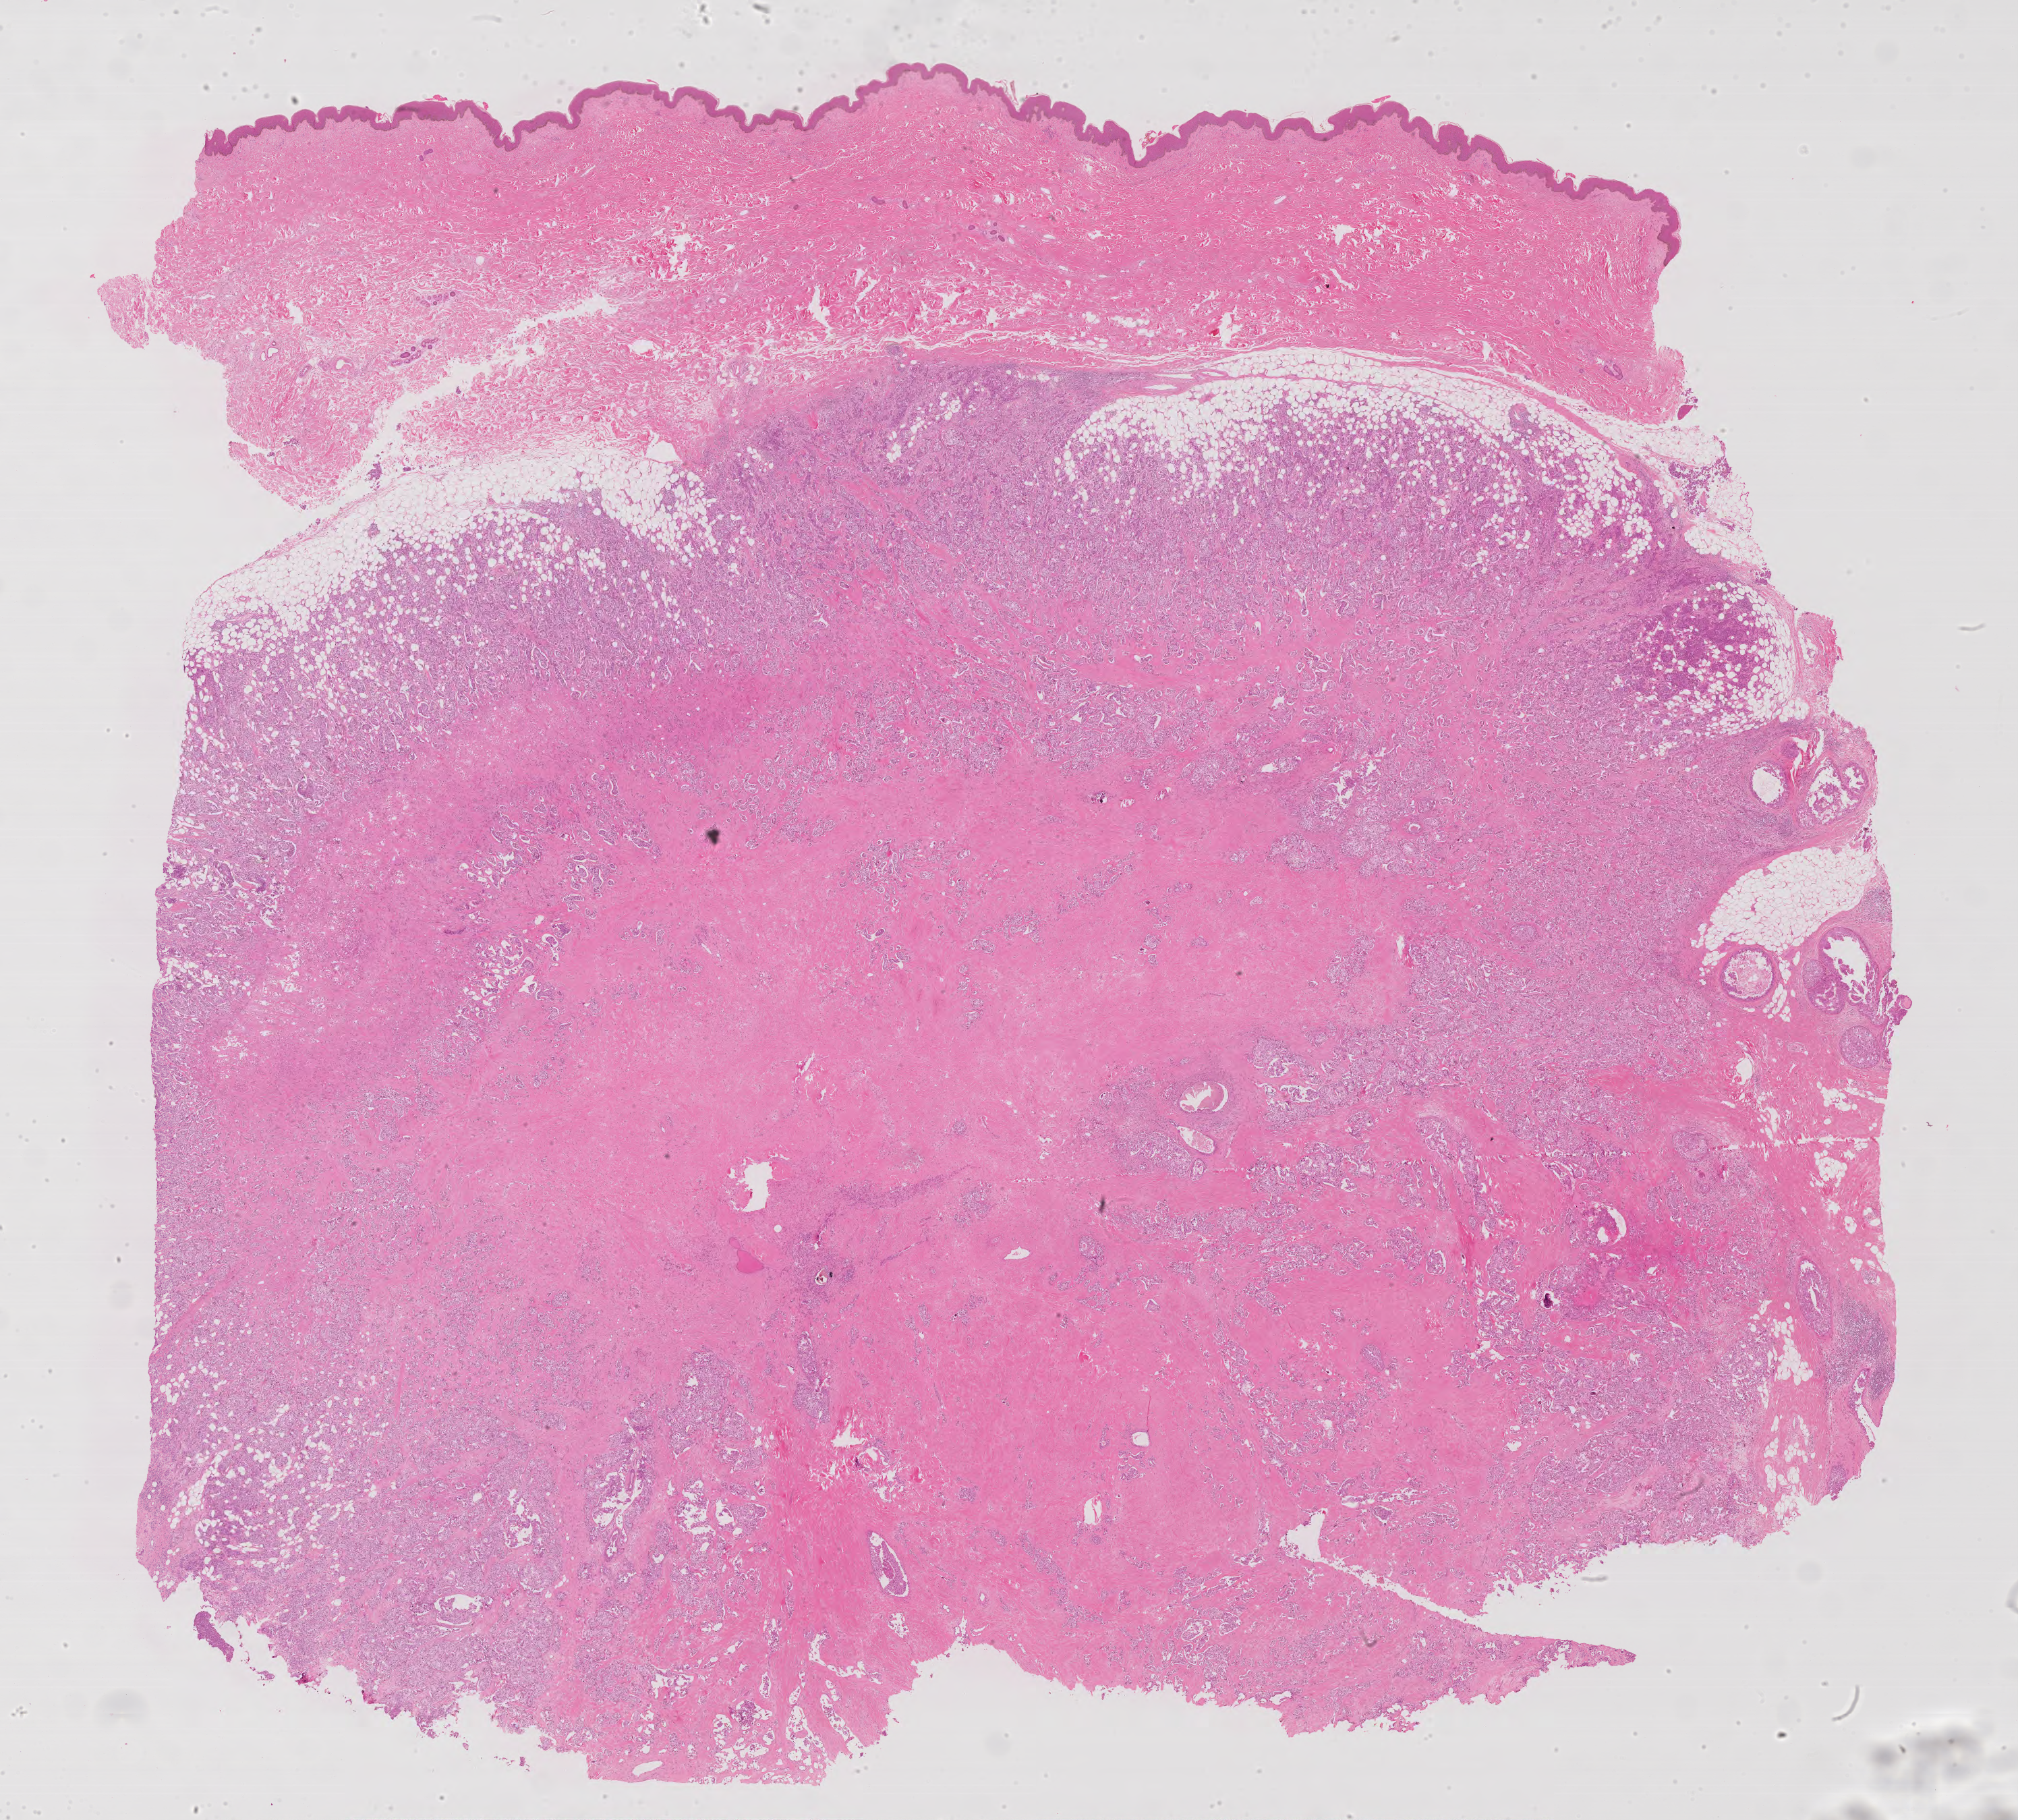
Whole-slide histology image, H&E — low-resolution overview of the scanned area, about 23.9 x 21.6 mm (slide scanned at 40x). Formalin-fixed paraffin-embedded (FFPE) diagnostic section. Breast, primary tumour sample. Patient: female, age at initial diagnosis 62 years.
Histologic diagnosis: Infiltrating duct carcinoma, NOS. AJCC pathologic stage: IIB (7th edition).